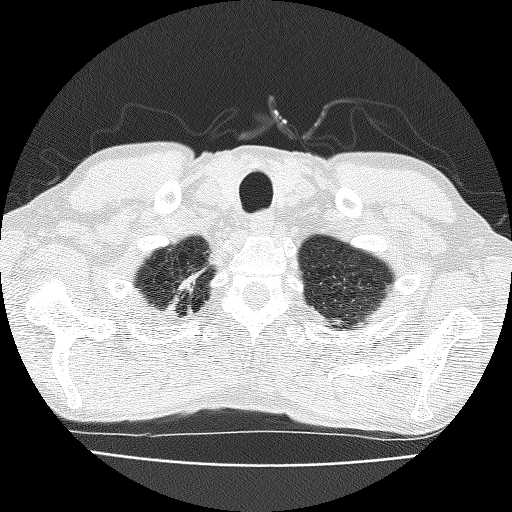
Axial slice from a low-dose chest CT screening exam, third screening round (two years after baseline), lung window (W 1500 / L -600 HU), 2 mm slice thickness, lung (sharp) reconstruction kernel (FC51), 120 kVp, slice 23 of 185 in the series. Male, age 63 years at enrolment. Current smoker at enrolment.
• Lesion marked by an expert reader, bounding box <147,258,228,323> (left, top, right, bottom; pixels).
• Screening reader's record for this exam (one nodule recorded; not confirmed to be the boxed lesion): non-calcified nodule or mass ≥4 mm, right upper lobe, 17 × 10 mm, spiculated (stellate) margins, soft tissue attenuation, pre-existing on the prior screen: yes; interval growth: yes.
• Official screen result: positive, other.